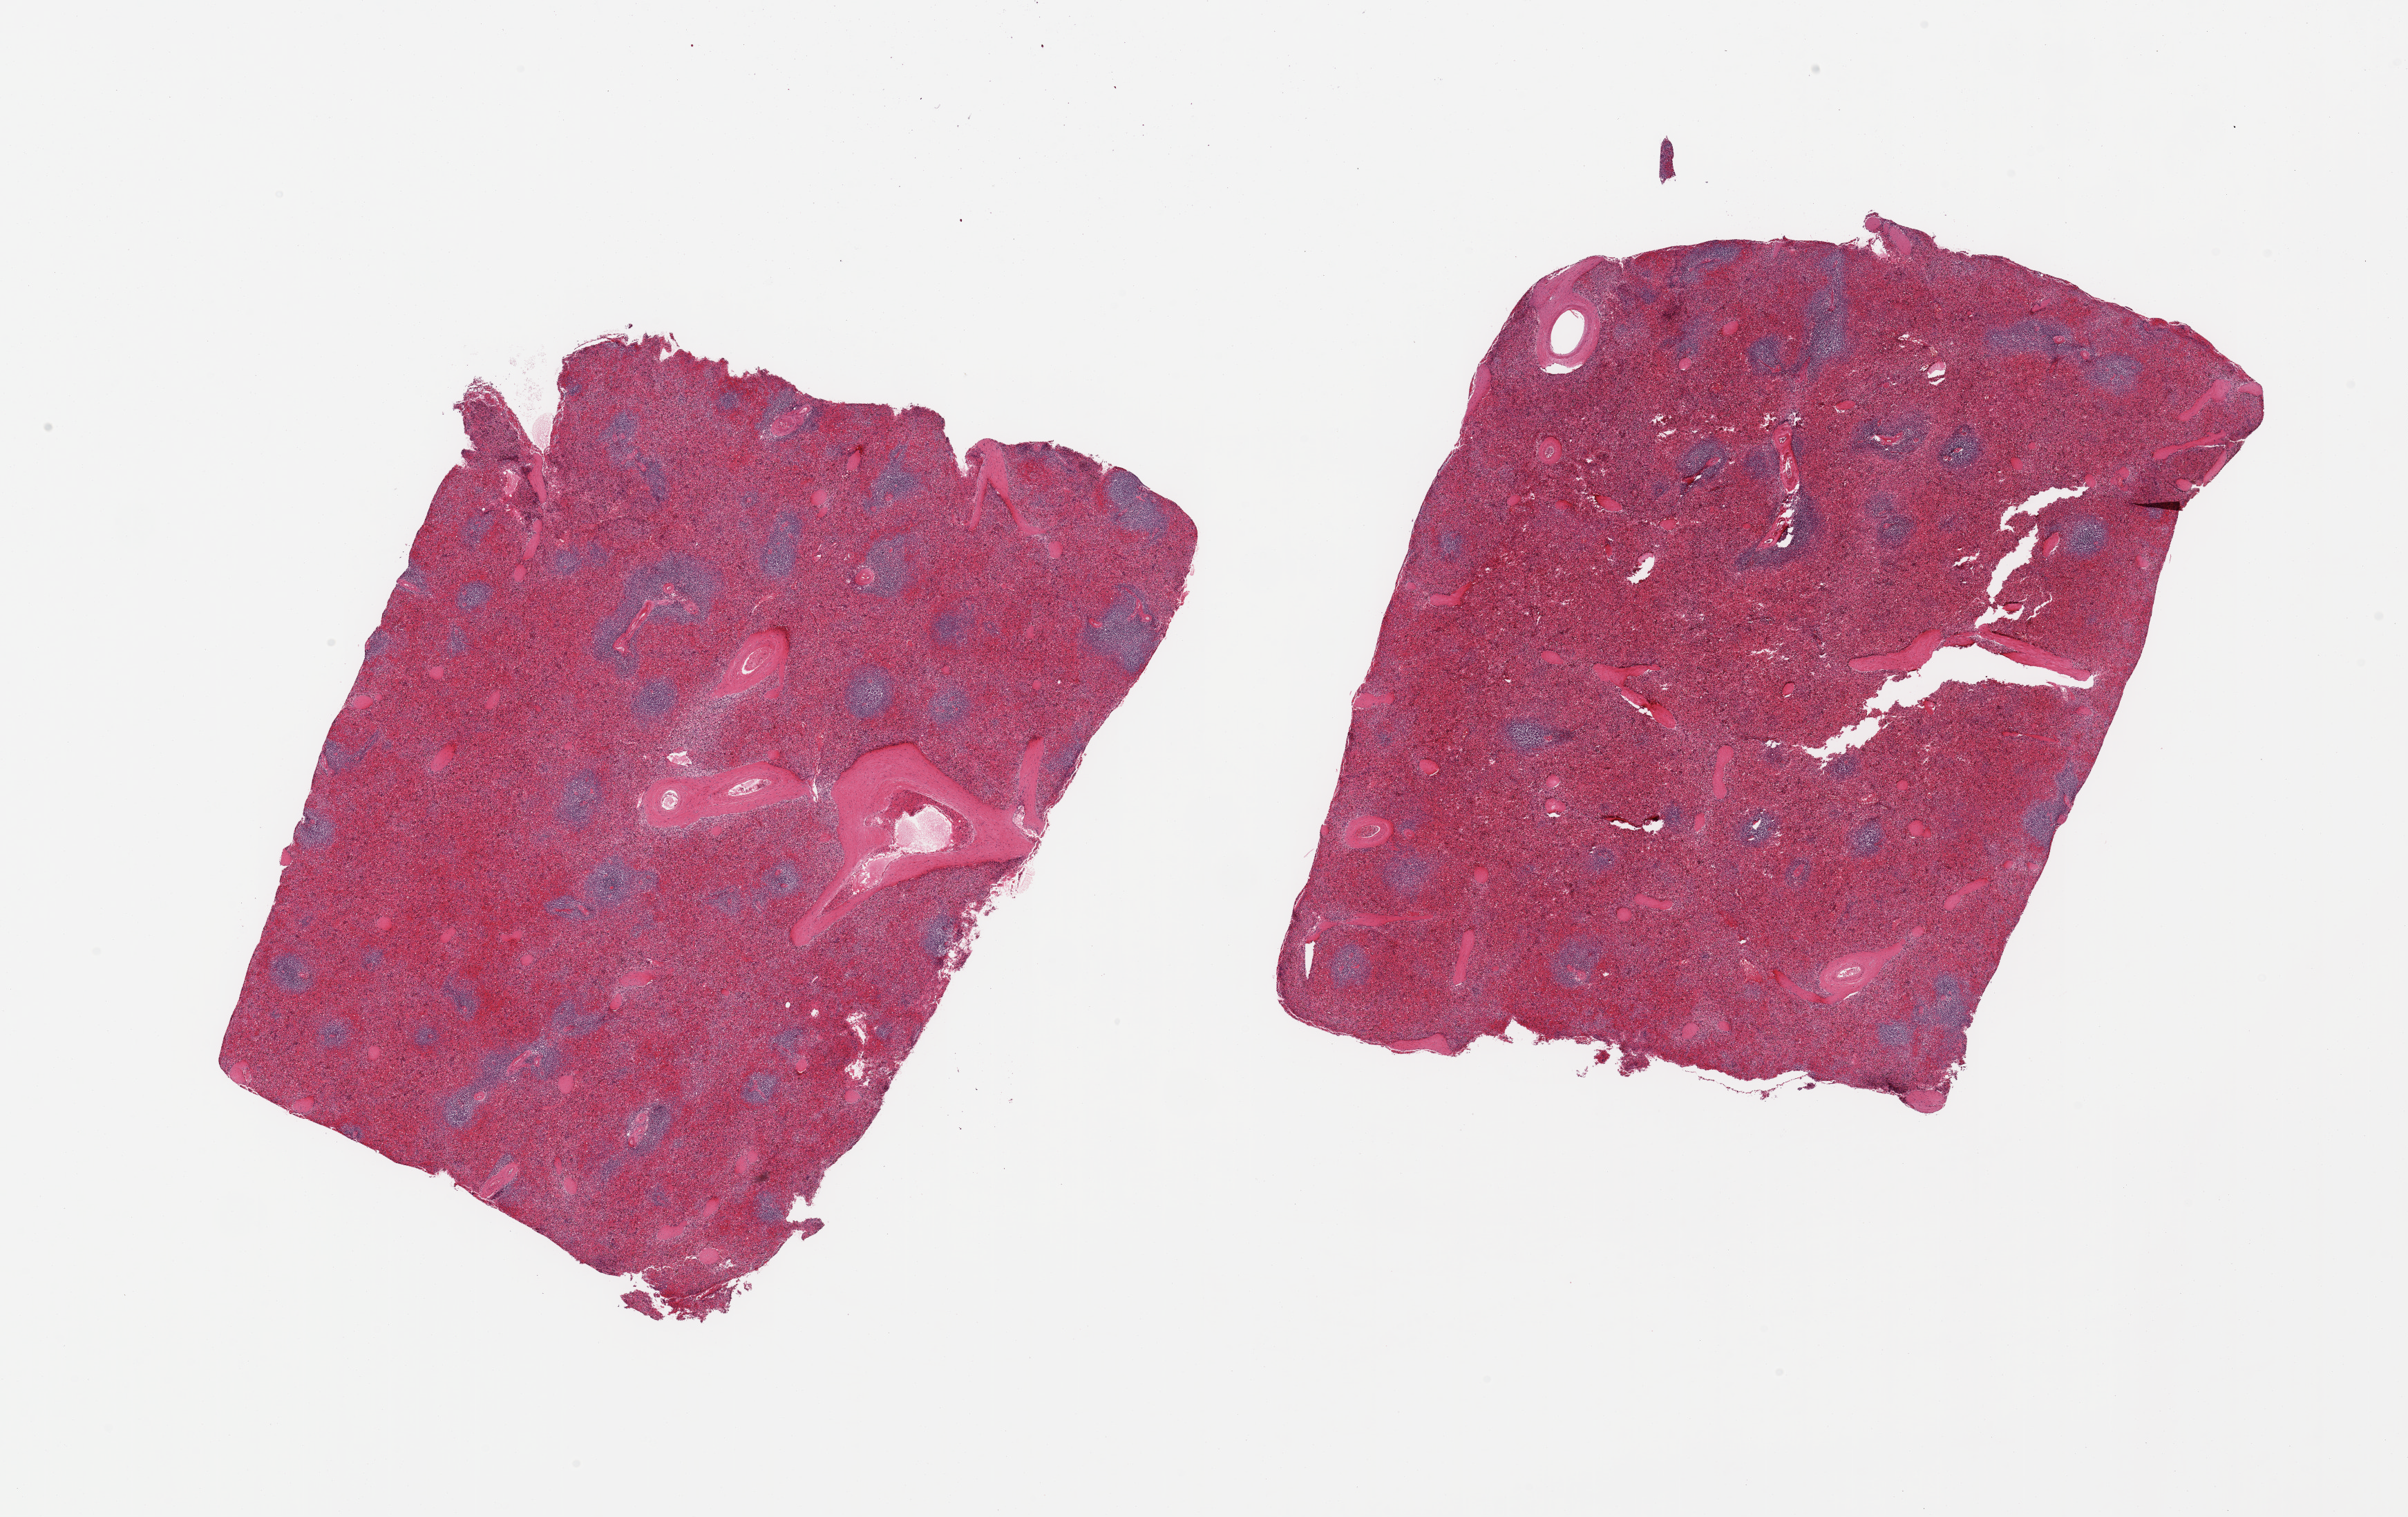
Digitized hematoxylin and eosin (H&E)-stained section — low-resolution overview of the scanned area, about 27.6 x 17.4 mm (slide scanned at 20x), PAXgene-fixed paraffin-embedded (PFPE) section, sampled site (target tissue): spleen, tissue donor sample. Donor sex: male.
Review note (as recorded): 2 pieces, moderate congestion.